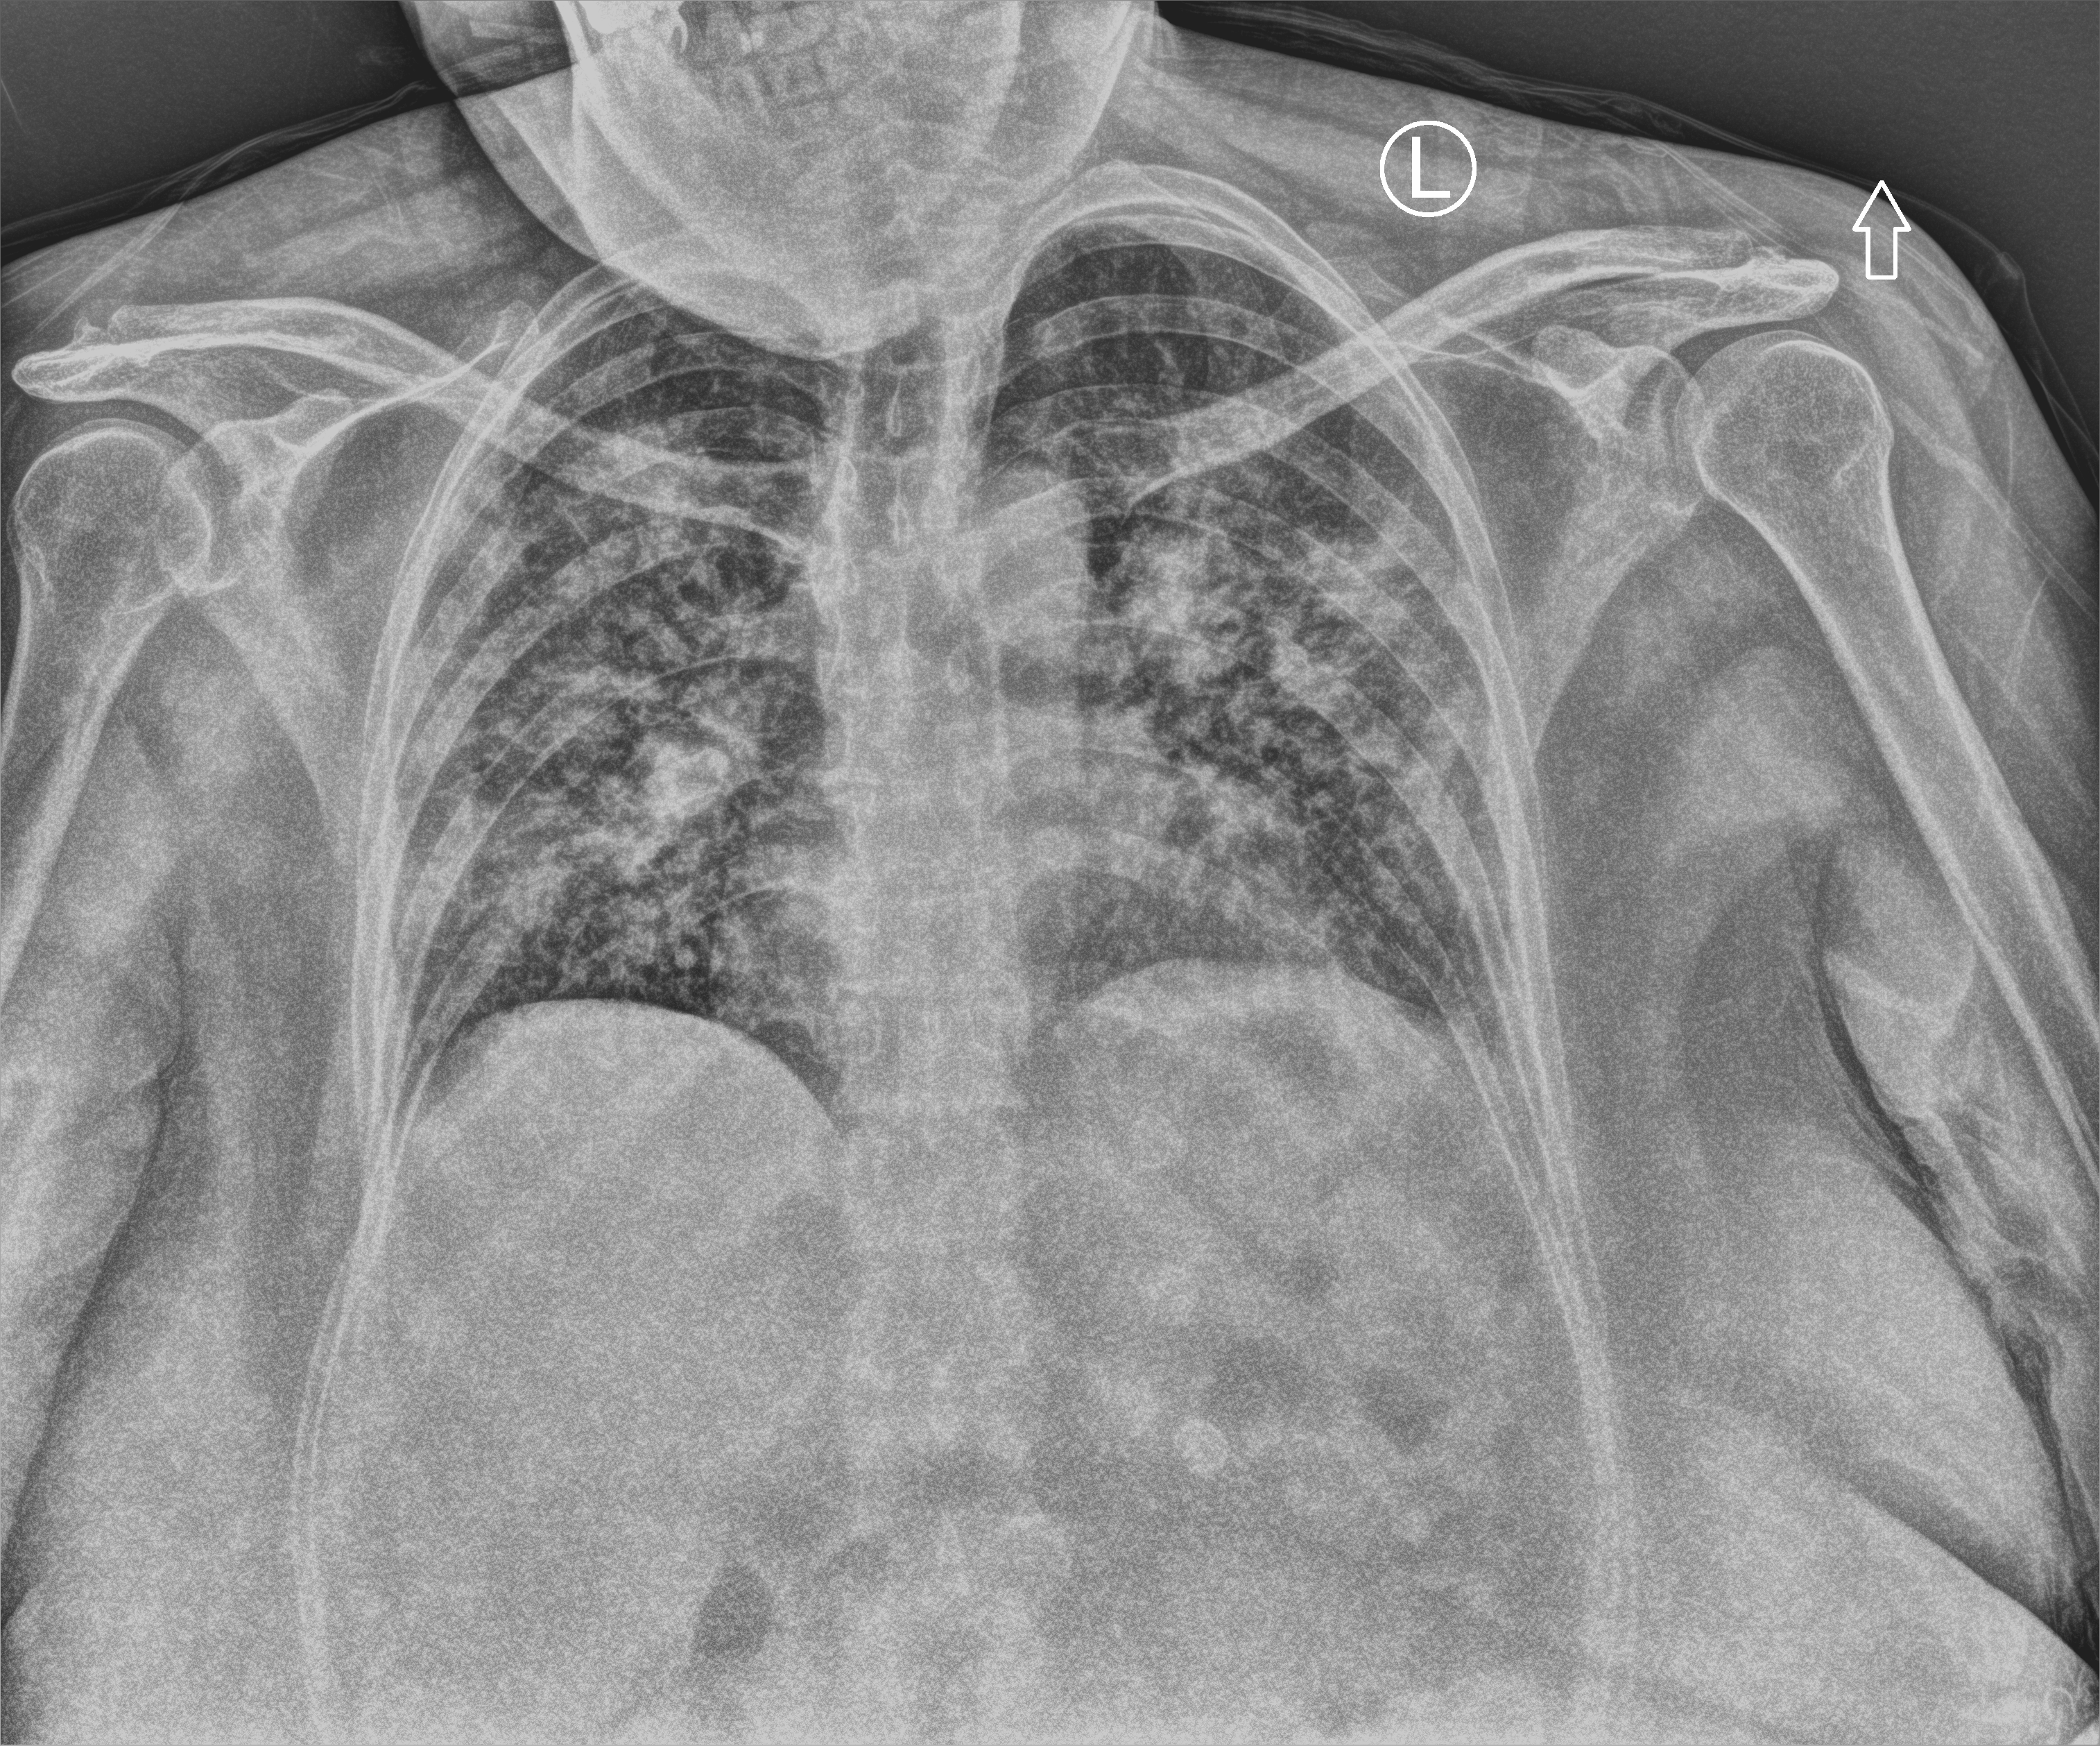
Bedside chest radiograph (computed radiography), anteroposterior (AP) projection. Patient hospitalised with COVID-19; female, aged 18–59 years.
Admission-level facts for this patient (not findings on this image; timing relative to this image not recorded):
- mechanically ventilated during this hospital stay: no